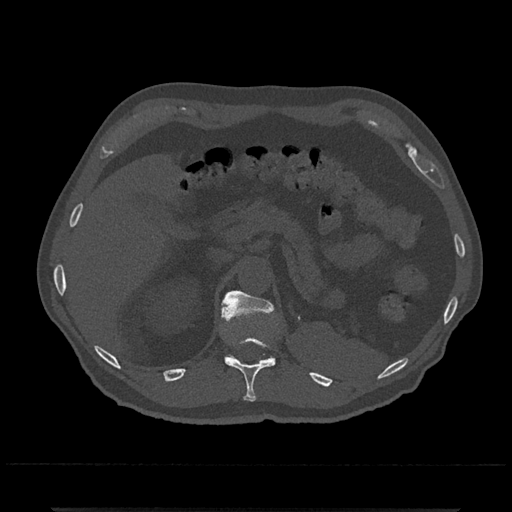
CT including the spine, one axial slice; position 469 of 797 along the scan axis; 120 kVp; bone window (W 1800 / L 400 HU); 512 × 512 image matrix, field of view 393 × 393 mm. Male patient, age 67 years. From the clinical record (not read from this slice): primary cancer: prostate.
Annotated regions visible in this slice (semi-automatically segmented with operator editing):
- T11 vertebra: bounding box [x1, y1, x2, y2] px = [225, 336, 276, 402]
- T12 vertebra: [221, 291, 276, 360]